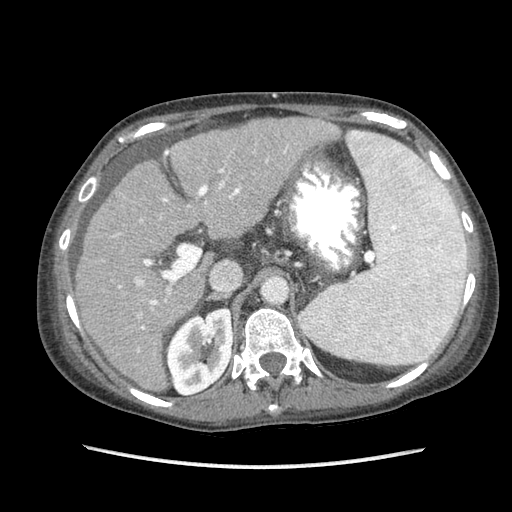
Contrast-enhanced abdominal CT (liver protocol), one axial slice; position 54 of 87 along the scan axis; soft-tissue window (W 400 / L 40 HU); 2.5 mm slice thickness; 512 × 512 image matrix. Case-level facts recorded for this patient, not image findings: diagnosis: hepatocellular carcinoma (patient treated with transarterial chemoembolisation; whether this scan precedes or follows treatment is not stated here); TNM stage (as recorded): Stage-IIIB; Child-Pugh class: A; tumour differentiation: no biopsy; tumour nodularity: uninodular.
Outlined on this slice (semi-automatic segmentation, software-assisted and operator-edited):
- liver parenchyma outside the tumour (the mass and vessels are separate outlines, so this box may not span the whole liver): box from (x=76, y=117) to (x=382, y=390) px
- liver vessels: (x=113, y=131)–(x=380, y=352)